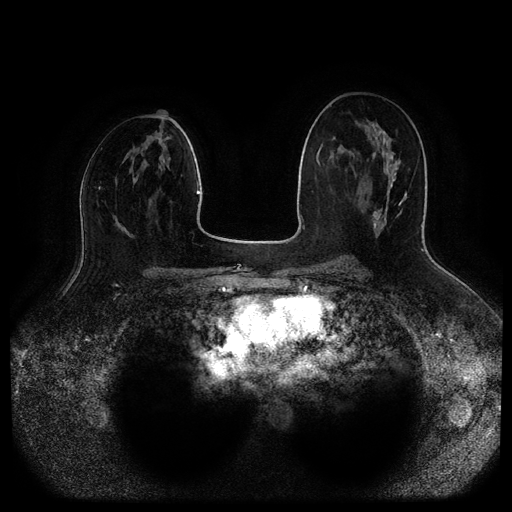
Breast MRI (dynamic contrast-enhanced, multi-phase), one axial slice; position 50 of 116 along the scan axis; dynamic contrast-enhanced series, time point 2 of 5 at this slice position (early post-contrast); 1.5 T; TE 2.6 ms, TR 5.2 ms; 512 × 512 image matrix, field of view 380 × 380 mm. Female patient, age 45 years.
Annotated regions visible in this slice (semi-automatically segmented with operator editing):
- breast lesion (labelled benign in the annotation): bounding box (x1, y1, x2, y2) in pixels: (372, 137, 397, 238)